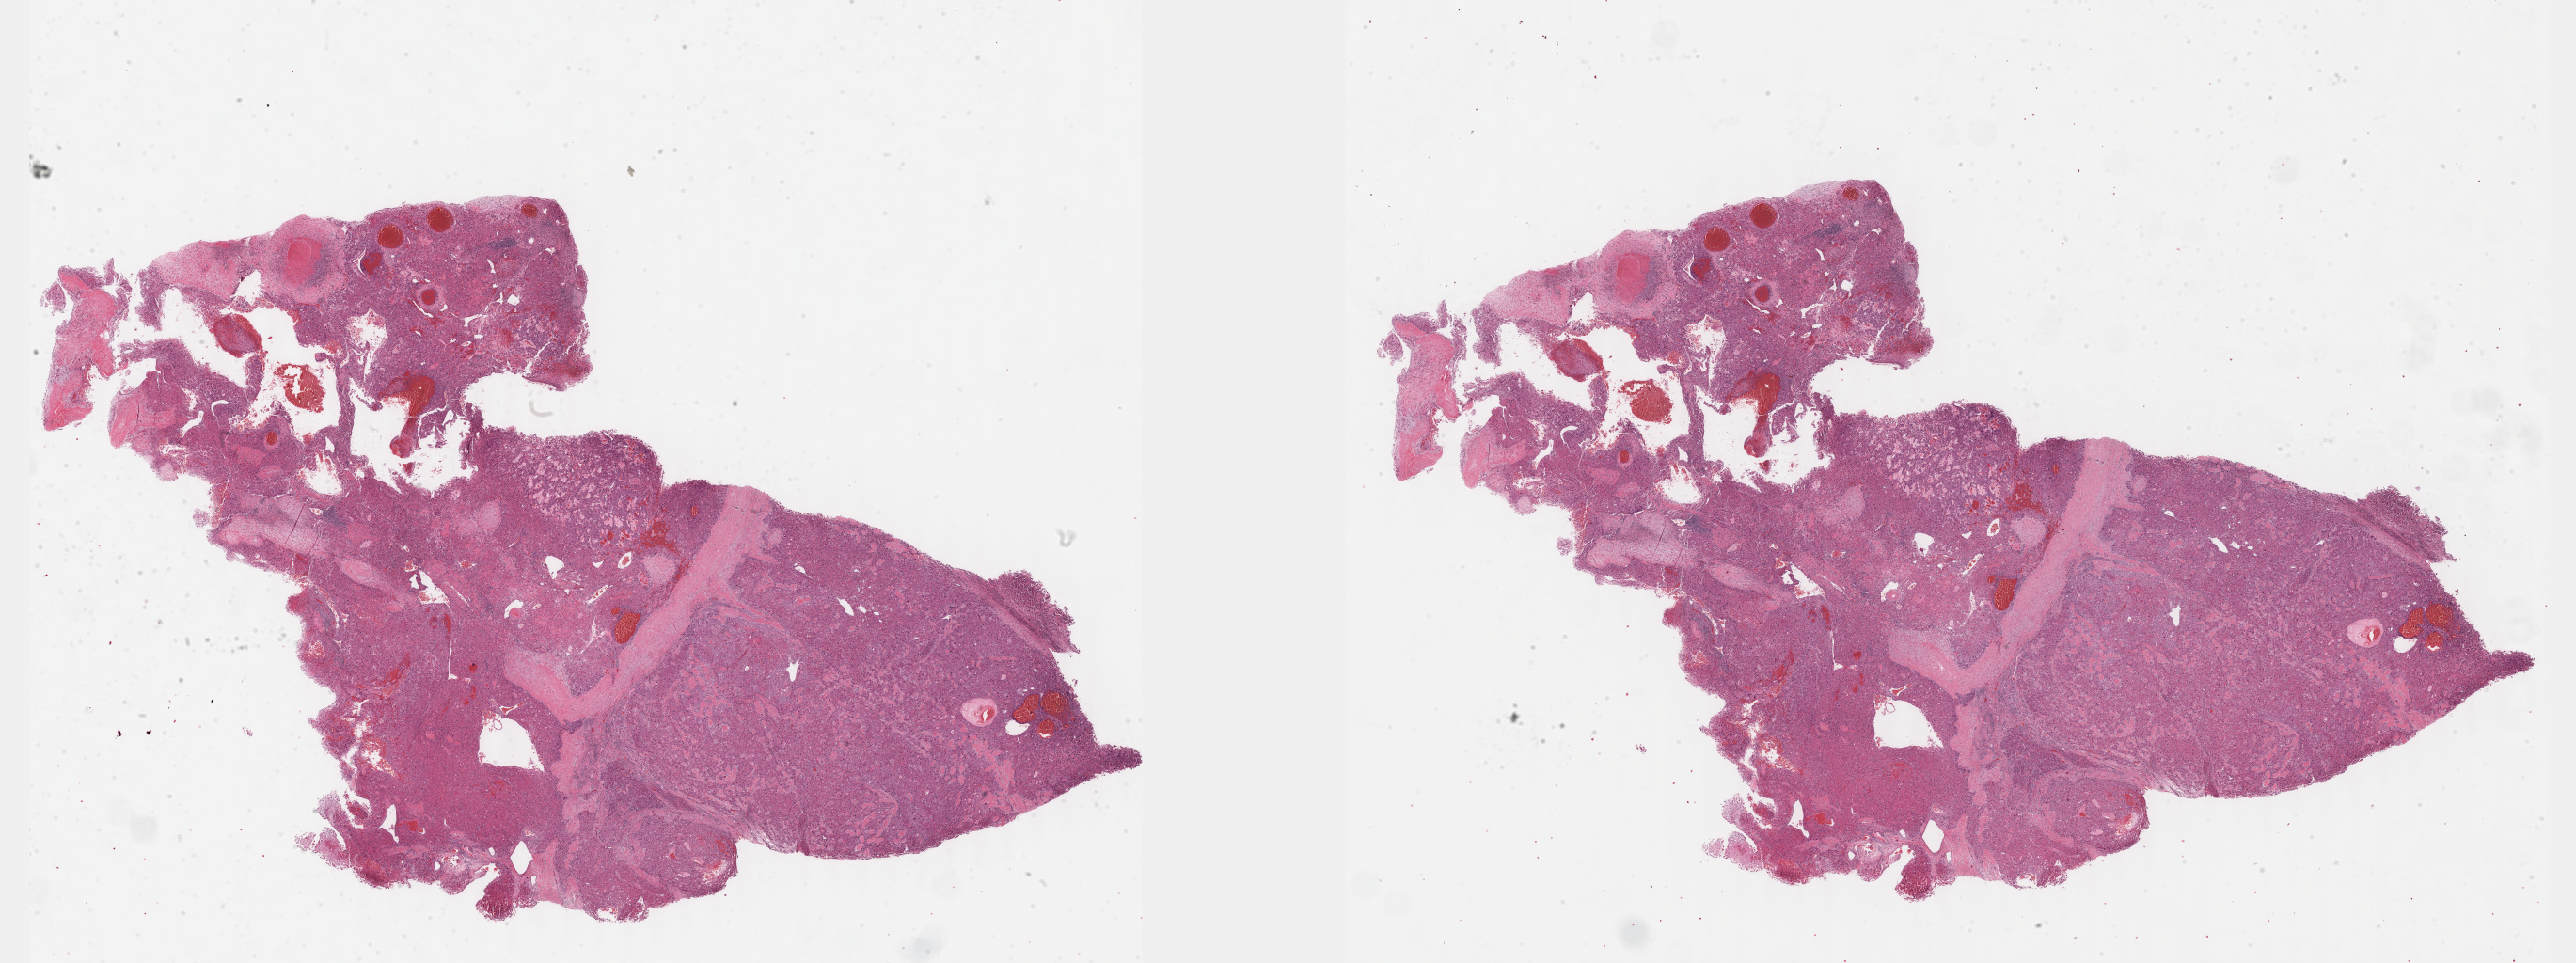
Whole-slide histology image, H&E-stained — a low-resolution overview of the entire scanned area, about 44.3 x 16.5 mm (slide scanned at 40x), formalin-fixed paraffin-embedded (FFPE) diagnostic section, sample: primary tumour, liver. Male patient; age at initial diagnosis 34 years. Histologic grade: G3 (poorly differentiated).
• pathologic diagnosis: Hepatocellular carcinoma, fibrolamellar
• AJCC pathologic stage: I (7th edition)